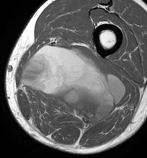
MRI of an extremity soft-tissue mass, one axial slice; slice 40 of 86 in the series (ordered by position); MR volume resampled by the dataset authors to the PET/CT grid (not the native acquisition matrix); 3.27 mm slice thickness; 147 × 158 image matrix. Male patient. Case-level facts recorded for this patient, not image findings: histological type: undifferentiated pleomorphic liposarcoma; grade: high; site of the primary tumour: left thigh.
Annotated regions visible in this slice (expert contour drawn on MRI and transferred to this co-registered scan by the dataset authors):
- gross tumour volume including surrounding oedema: box from (x=21, y=46) to (x=125, y=127) px
- gross tumour volume (mass): (x=21, y=46)–(x=125, y=127)